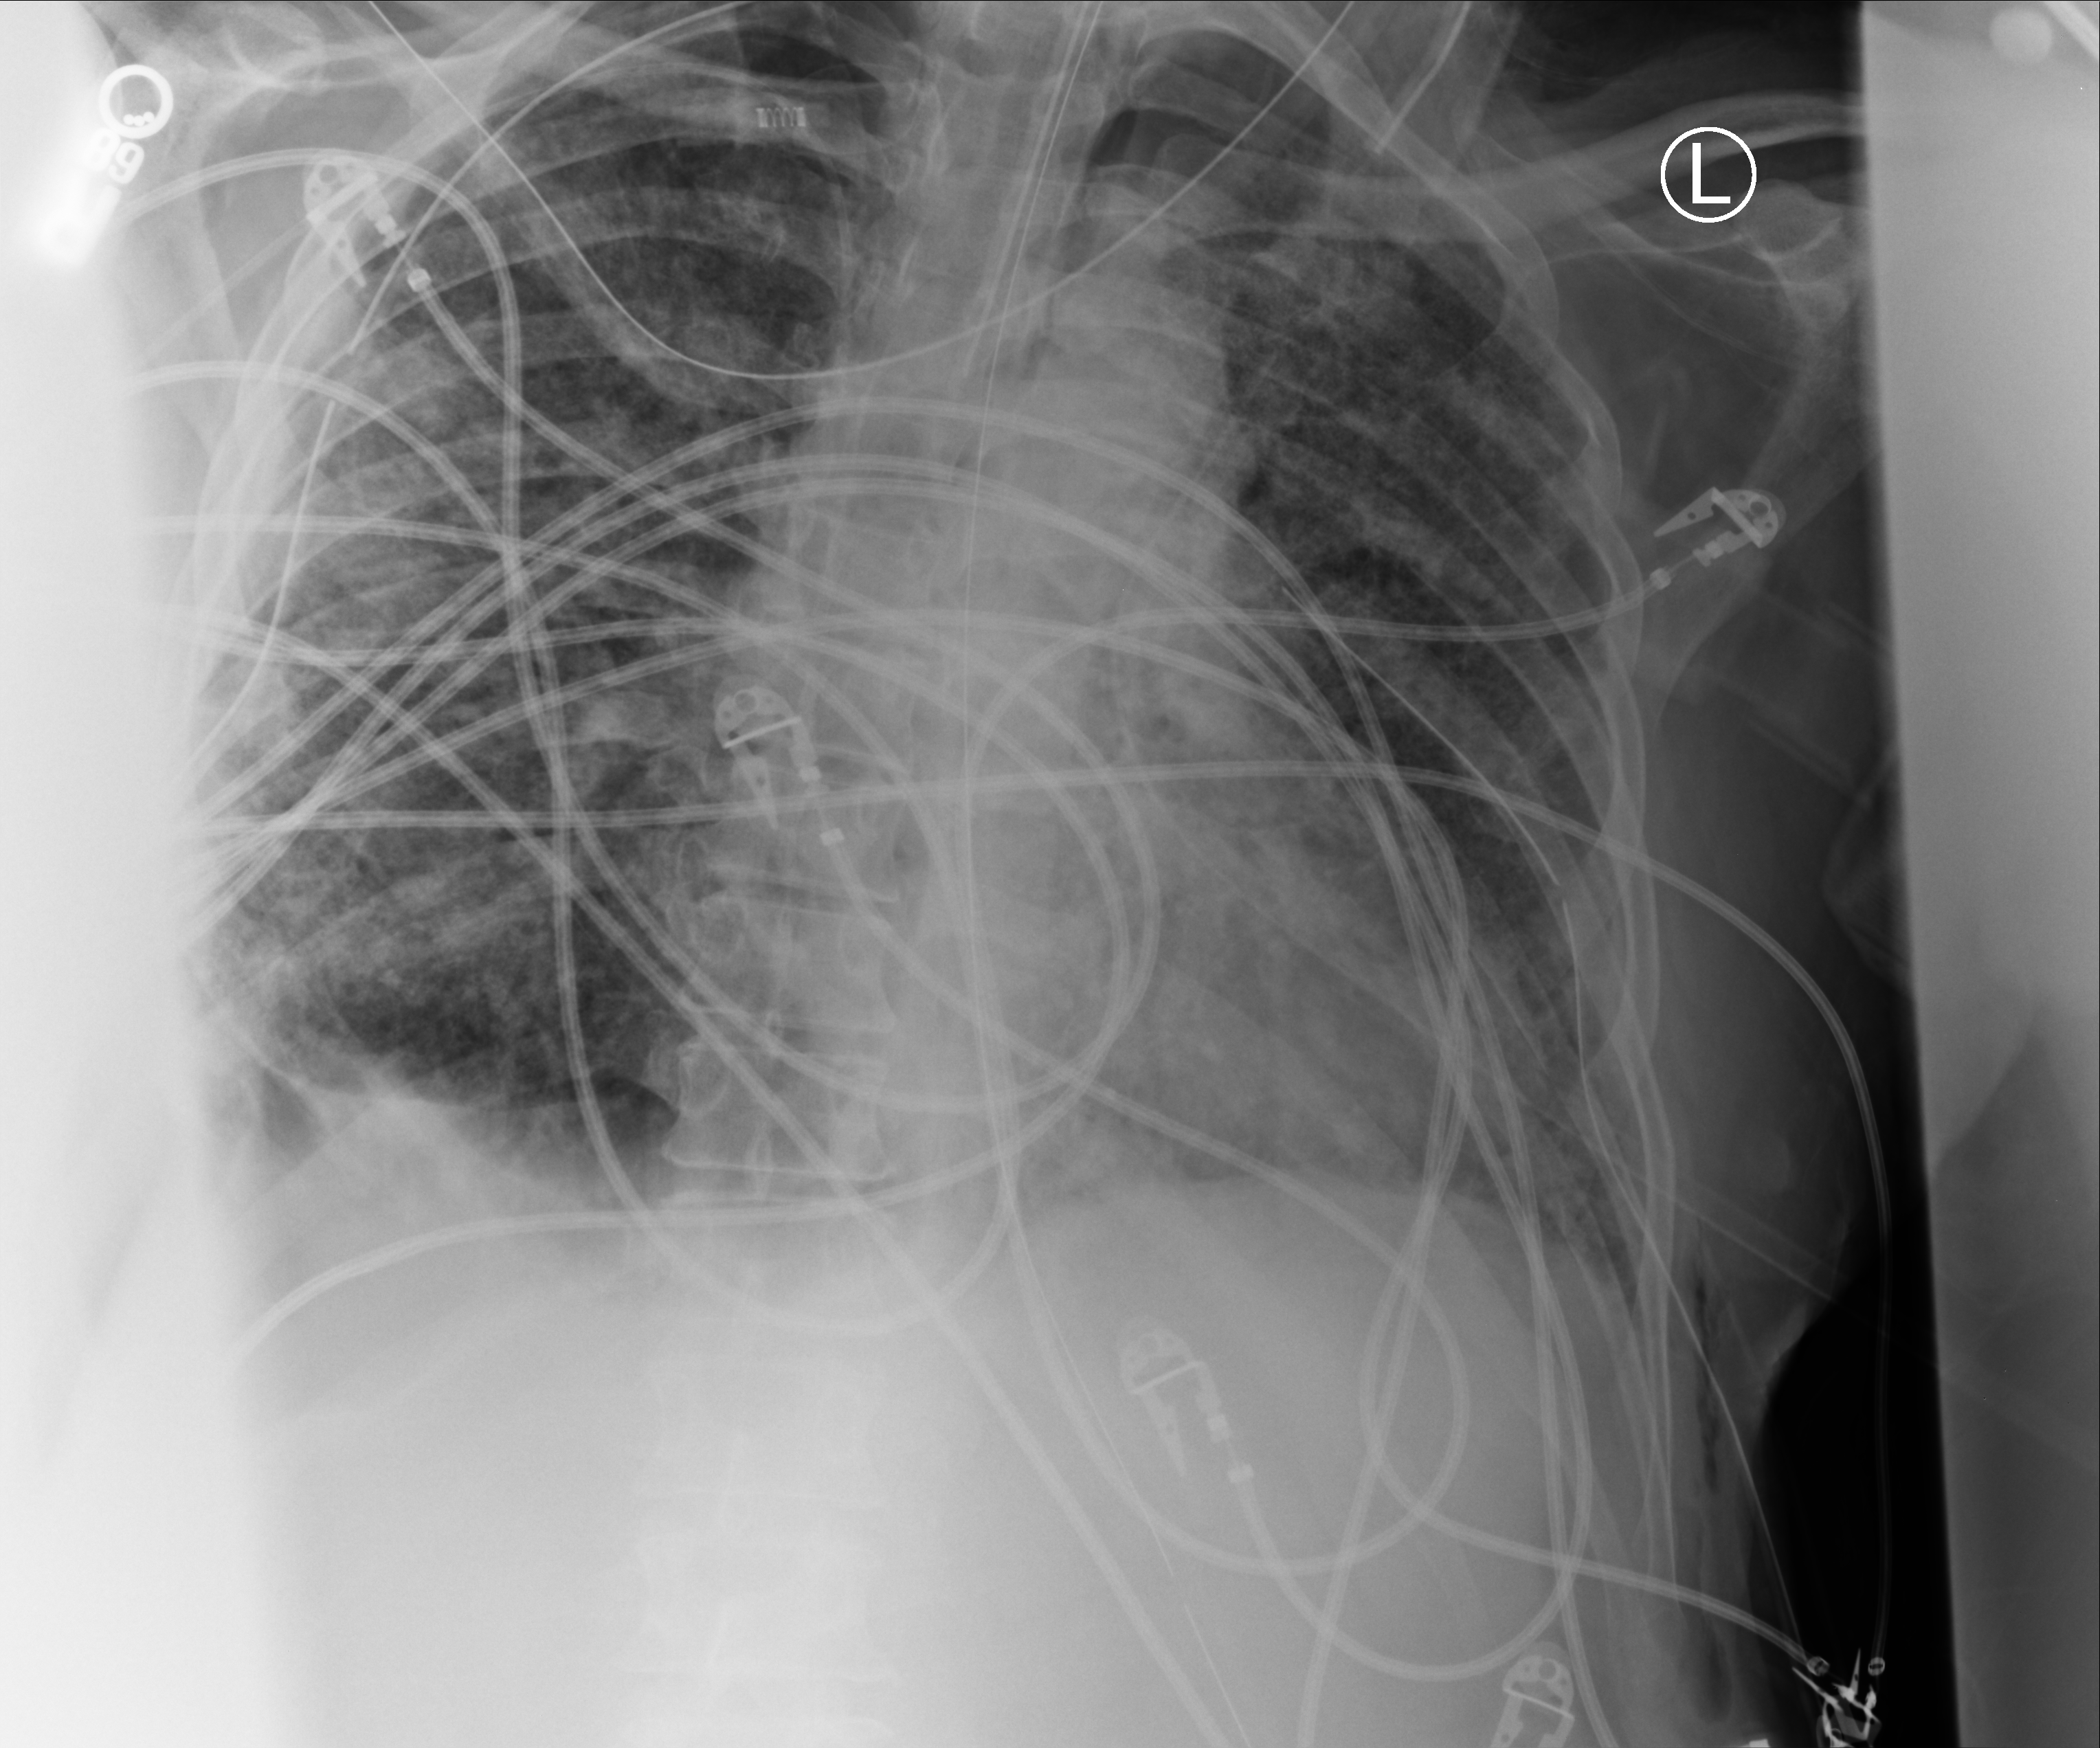
Chest X-ray (portable), anteroposterior (AP) projection. Male patient hospitalised with COVID-19, age 60–74 years.
Hospital-stay facts (about this admission, not read from this image; timing relative to this image not recorded): admitted to intensive care during this hospital stay: yes; mechanically ventilated during this hospital stay: yes; smoking status (admission record): never.